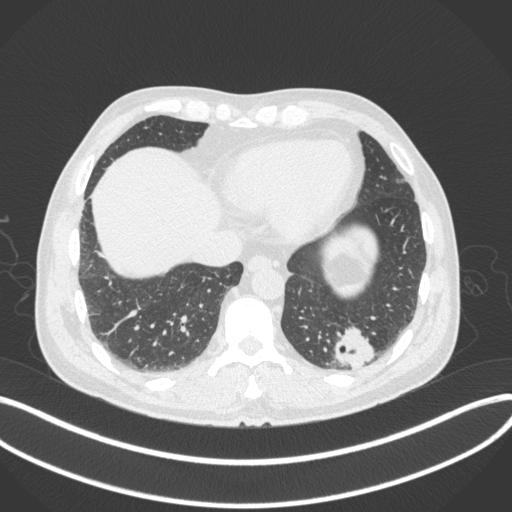
Chest CT, one axial slice. Position 67 of 313 along the scan axis. Reconstruction kernel B31f. 120 kVp. Lung window (W 1500 / L -600 HU). 1 mm slice thickness. 512 × 512 image matrix, field of view 400 × 400 mm. Male patient, age 54 years. Case-level facts recorded for this patient, not image findings: clinical TNM (as recorded): T1c N0 M1; histopathological grade: G3.
Outlined on this slice (rectangle marked by the reading radiologist):
- lung tumour (recorded histology: adenocarcinoma): box from (x=332, y=325) to (x=380, y=371) px